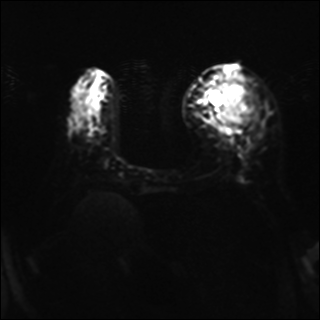
Breast MRI, one axial slice; position 12 of 37 along the scan axis; diffusion-weighted series; image 2 of 4 stored at this slice position (different b-values; order by instance number); 1.5 T; 320 × 320 image matrix, field of view 320 × 320 mm. Female patient.
Outlined on this slice (expert manual segmentation):
- tumour on diffusion-weighted imaging: box from (x=210, y=81) to (x=258, y=128) px